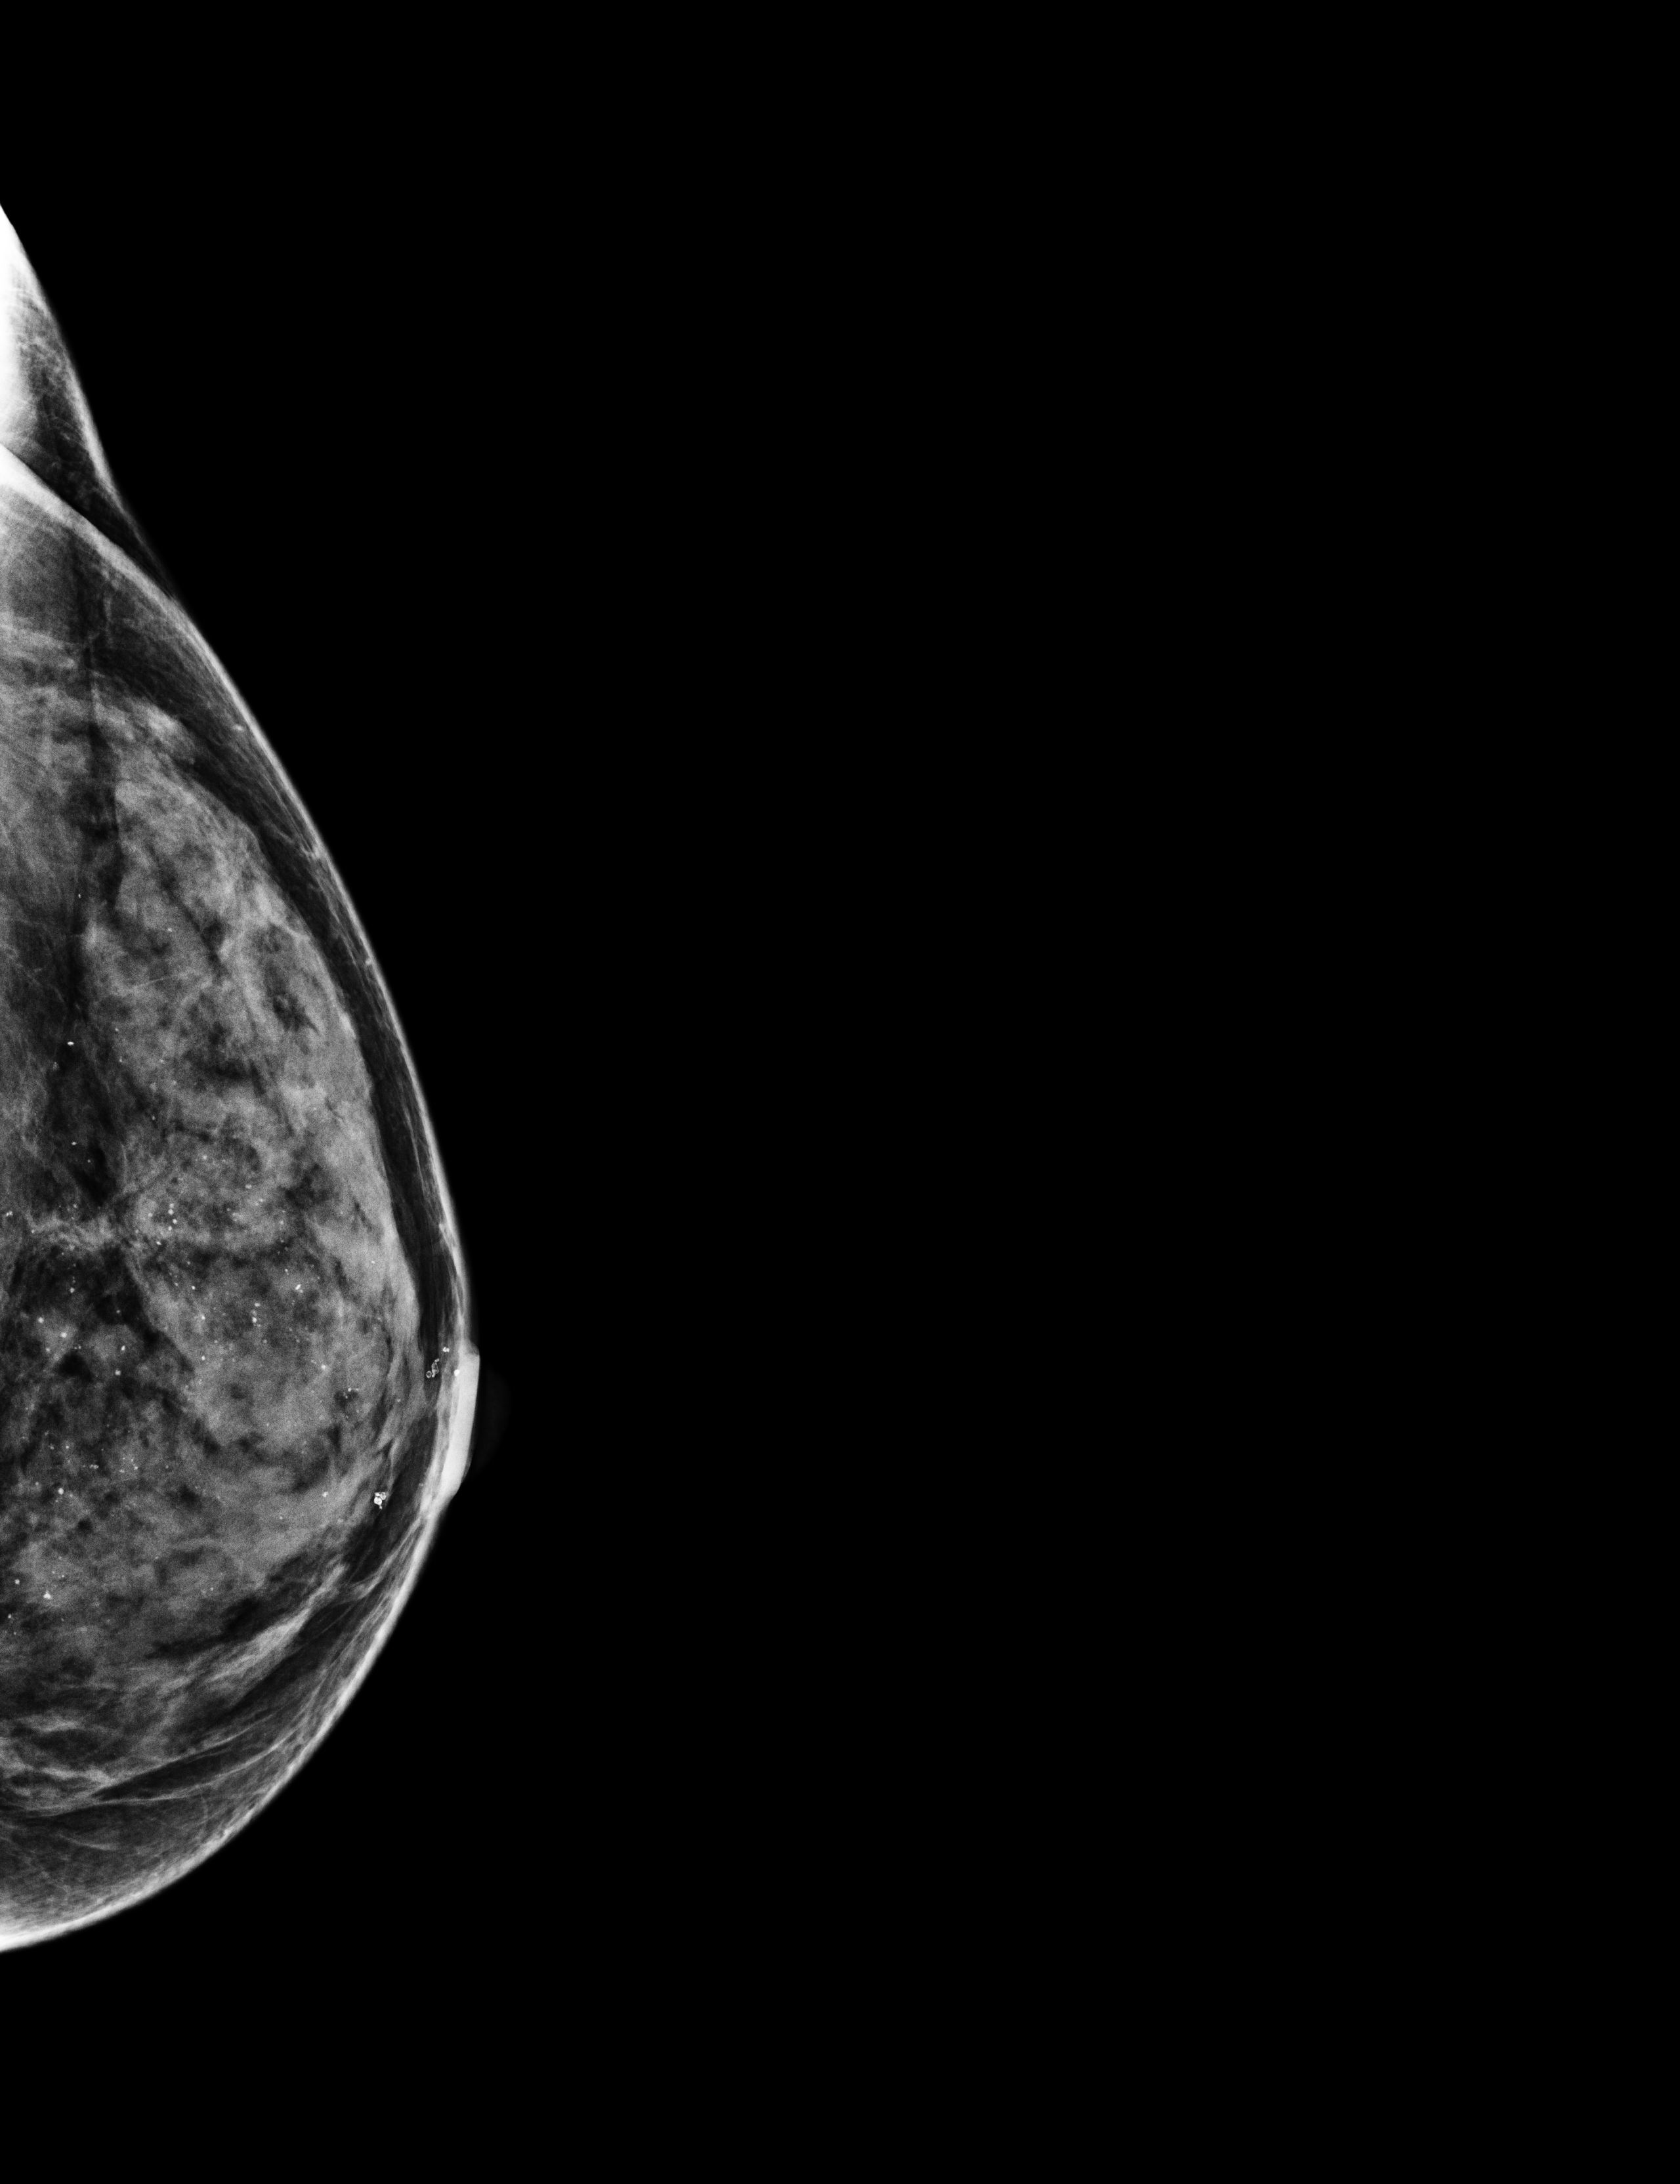
Full-field digital mammogram (FFDM); left breast; exaggerated CC view (lateral); screening examination; system: Selenia Dimensions. Patient: female, 49 years.
BI-RADS breast density category at the screening exam (both breasts, scale 1–4): 4.